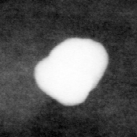
Region of interest cut from a scanned film mammogram (one marked finding); left breast; CC view.
Calcifications, morphology coarse; BI-RADS assessment category 2; benign without callback (not worked up further).